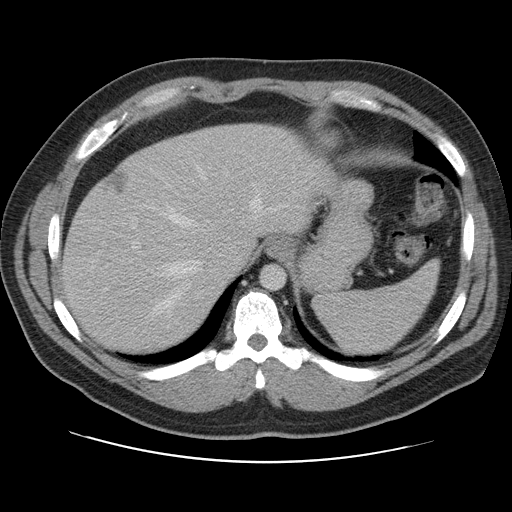
Contrast-enhanced abdominal CT, one axial slice. Slice 87 of 109 in the series (ordered by position). Intravenous contrast given. Soft-tissue window (W 400 / L 40 HU). 5 mm slice thickness. 512 × 512 image matrix. Male patient, age 35 years. Case-level facts recorded for this patient, not image findings: diagnosis: colorectal cancer liver metastases, imaged before liver resection; multiple liver metastases: yes.
Outlined on this slice (manually delineated by an expert):
- hepatic veins: box from (x=146, y=165) to (x=277, y=329) px
- liver: (x=63, y=124)–(x=323, y=354)
- planned liver remnant (the part of the liver to remain after resection): (x=63, y=124)–(x=322, y=354)
- portal vein (with intrahepatic branches): (x=126, y=167)–(x=211, y=271)
- liver metastasis: (x=108, y=171)–(x=128, y=194)